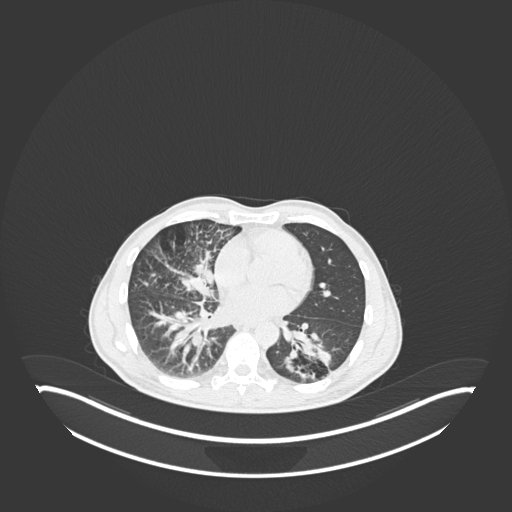
Chest CT, one axial slice; slice 103 of 237 in the series (ordered by position); reconstruction kernel B30f; 120 kVp; lung window (W 1500 / L -600 HU); 512 × 512 image matrix, field of view 500 × 500 mm. Male patient, age 49 years. From the clinical record (not read from this slice): clinical TNM (as recorded): T2b N1 M0.
Structures marked on this image (rectangle marked by the reading radiologist):
- lung tumour (recorded histology: adenocarcinoma): box from (x=276, y=325) to (x=334, y=382) px